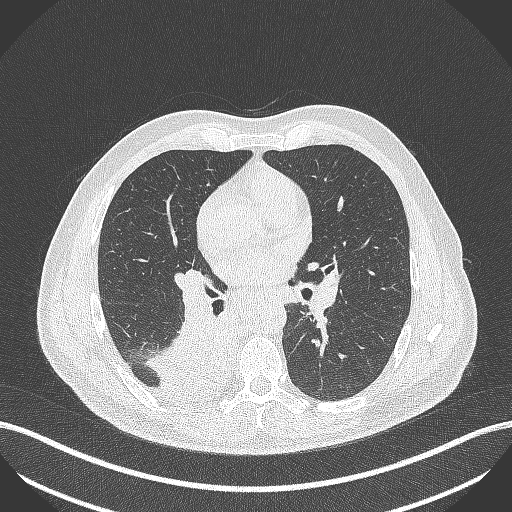
Chest CT, one axial slice. Slice 251 of 451 in the series (ordered by position). Lung window (W 1500 / L -600 HU). 1 mm slice thickness. 512 × 512 image matrix, field of view 400 × 400 mm. Patient: male, 61 years. Case-level facts recorded for this patient, not image findings: clinical TNM (as recorded): T1 N0 M0.
Outlined on this slice (bounding box drawn by a radiologist):
- lung tumour (recorded histology: small cell carcinoma): box from (x=144, y=305) to (x=239, y=401) px